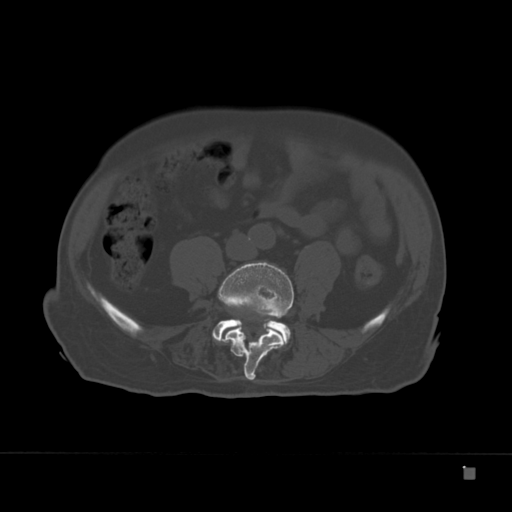
CT including the spine, one axial slice; position 37 of 332 along the scan axis; reconstruction kernel Br40s; 120 kVp; bone window (W 1800 / L 400 HU); 1.5 mm slice thickness; 512 × 512 image matrix, field of view 389 × 389 mm. Male patient, age 72 years. From the clinical record (not read from this slice): primary cancer: skeletal.
Outlined on this slice (semi-automatically segmented with operator editing):
- L4 vertebra: box from (x=222, y=262) to (x=294, y=381) px
- L5 vertebra: (x=212, y=318)–(x=291, y=345)